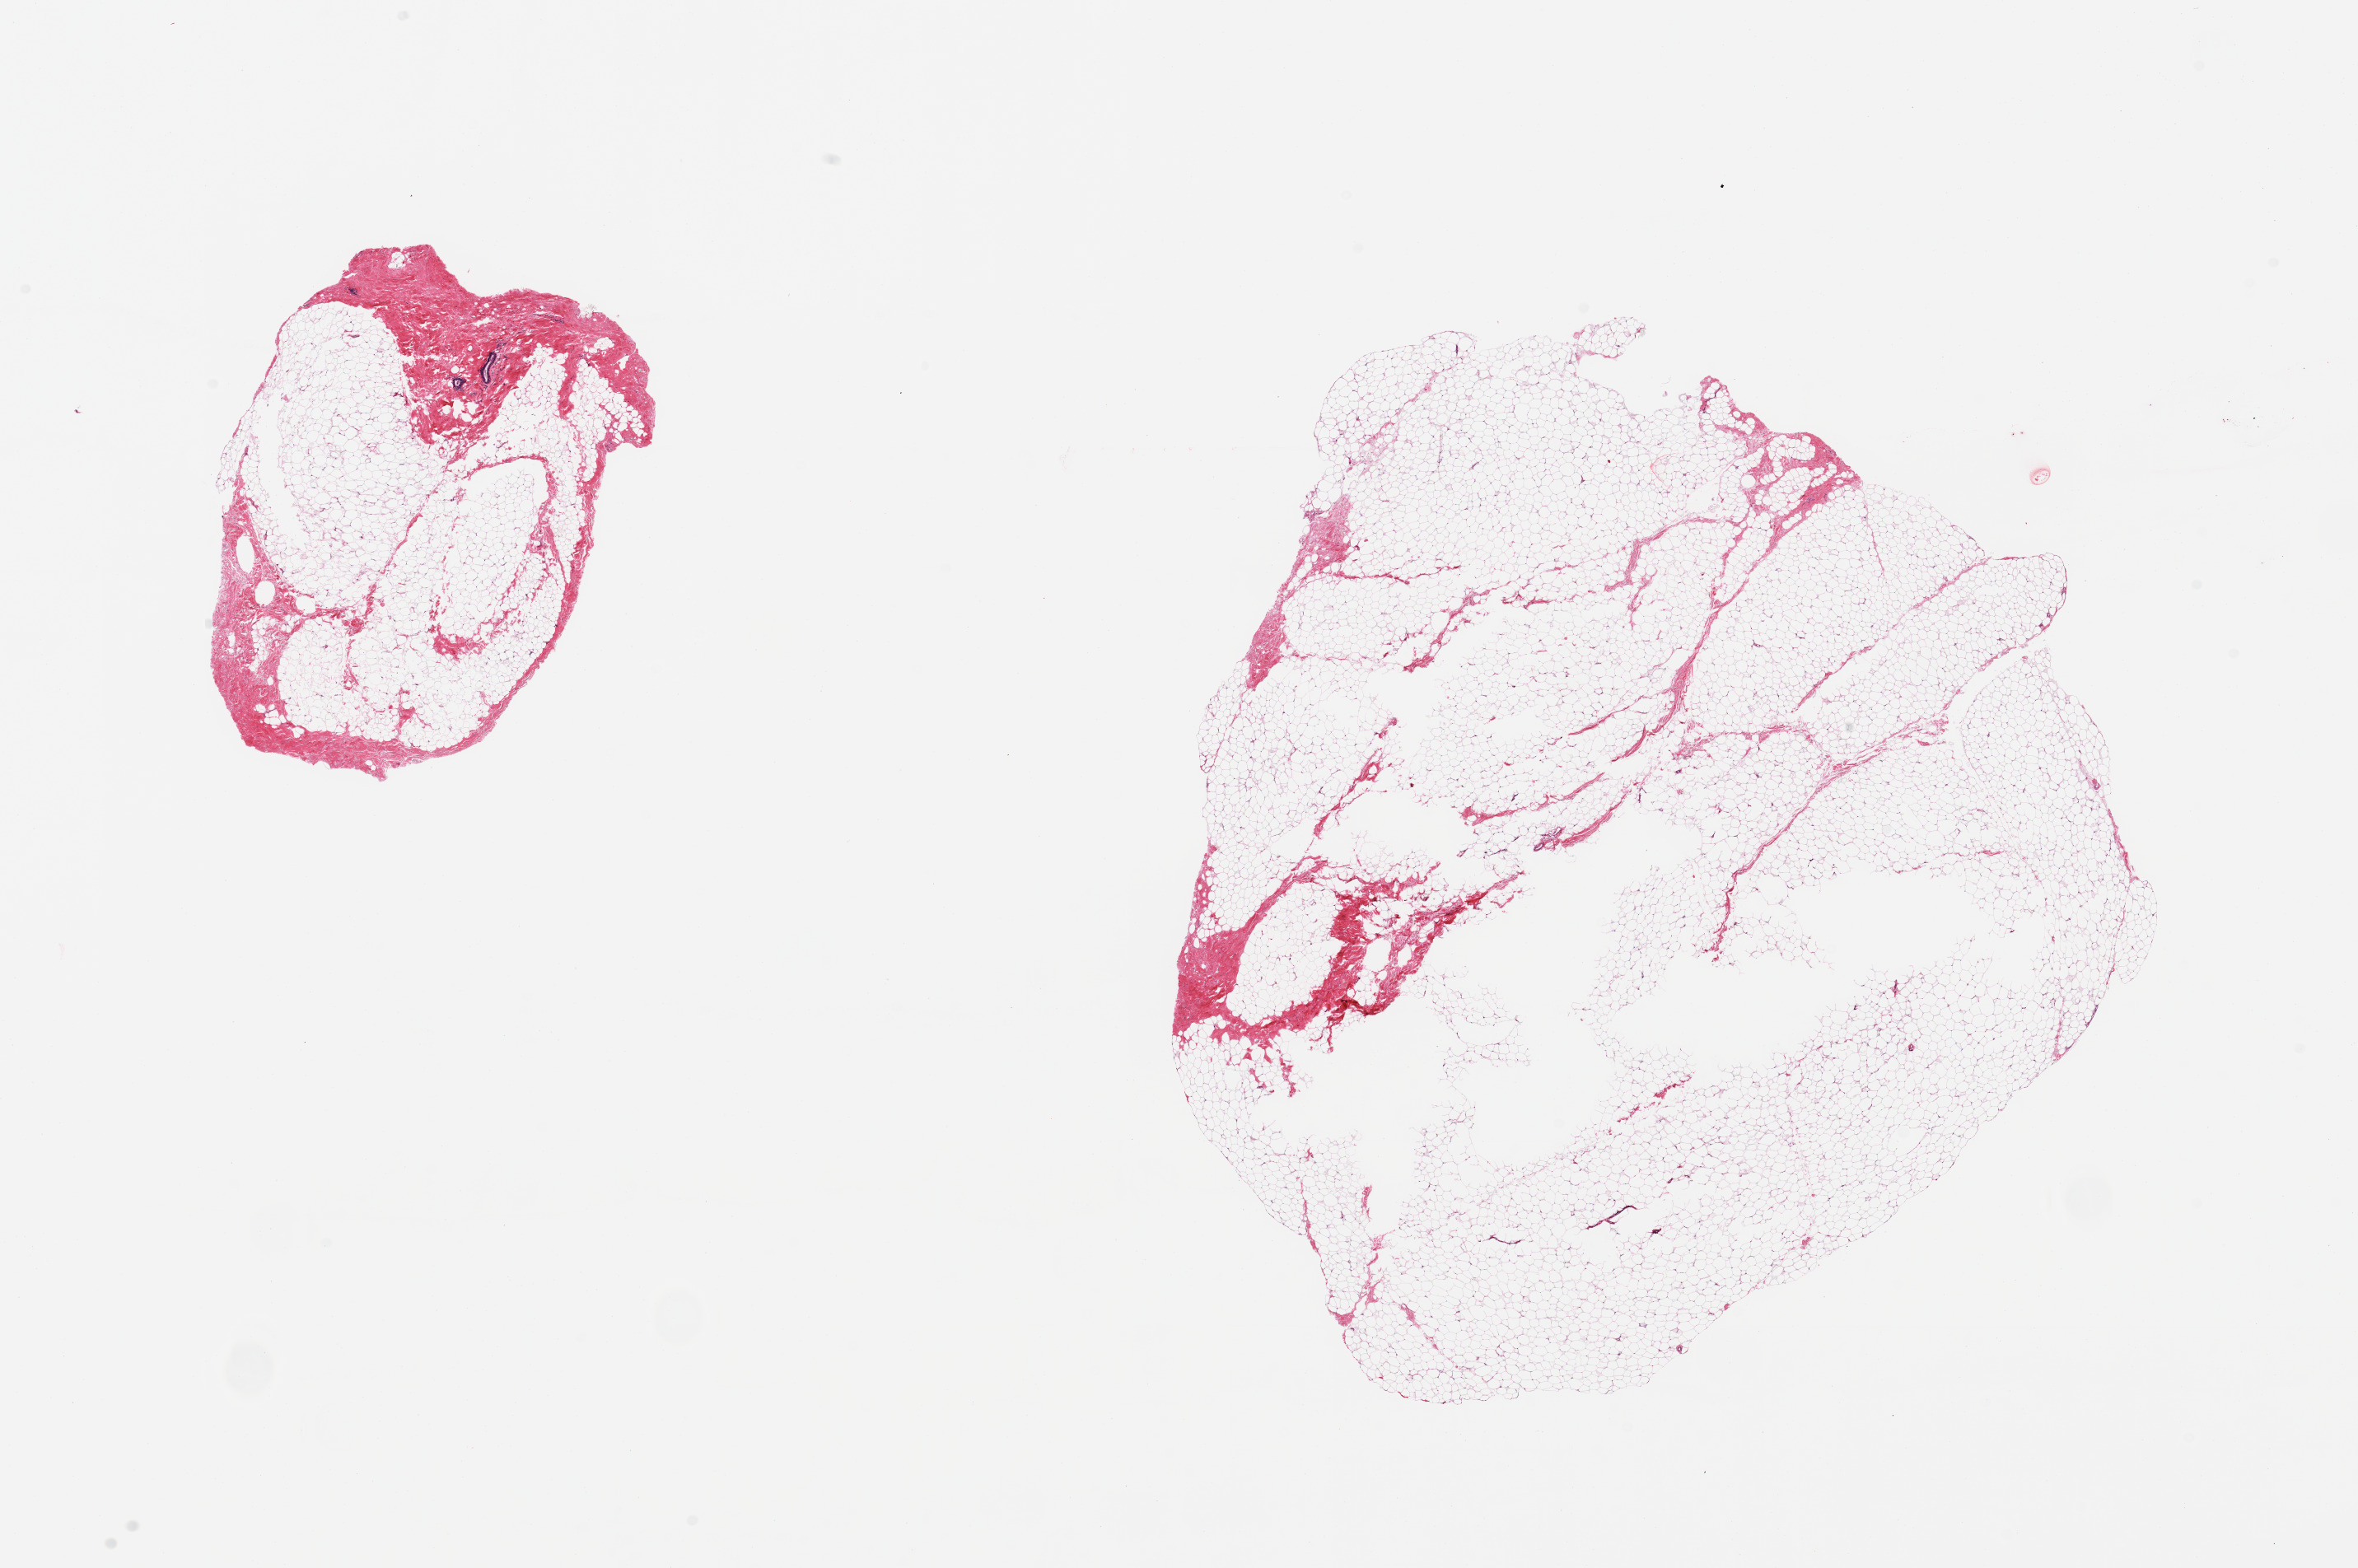
Whole-slide image, haematoxylin and eosin stain — shown as a low-resolution overview of the whole scanned area (about 22.6 x 15.1 mm, from a 20x scan); PAXgene-fixed, paraffin-embedded tissue; target tissue: breast; donor tissue sample. Donor sex: male.
* pathologist's review note for this sample: 2 pieces; 70 and 90% fat with stroma and rare duct